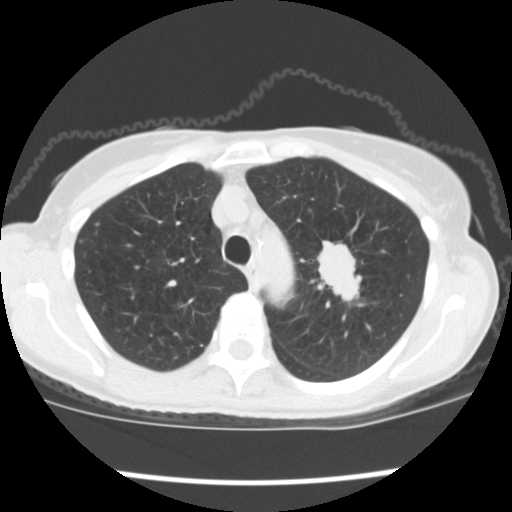
Low-dose screening chest CT, one axial slice. Position 140 of 176 along the scan axis. 120 kVp. Lung window (W 1500 / L -600 HU). 2.5 mm slice thickness. 512 × 512 image matrix, field of view 318 × 318 mm.
Structures marked on this image (outlined manually by an expert reader):
- lesion 1 (tumor, upper lobe of left lung): bounding box (x1, y1, x2, y2) in pixels: (317, 241, 362, 306)